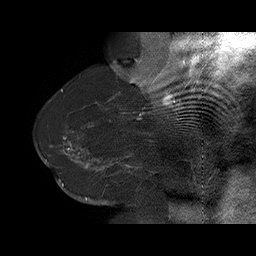
Breast MRI (dynamic contrast-enhanced), one sagittal slice. Slice 48 of 75 in the series (ordered by position). Dynamic contrast-enhanced series, time point 2 of 6 at this slice position (early post-contrast). 1.5 T. TE 4.5 ms, TR 32.4 ms. 3 mm slice thickness. 256 × 256 image matrix, field of view 180 × 180 mm. Female patient. From the clinical record (not read from this slice): setting: breast cancer imaged before/during neoadjuvant chemotherapy; receptor status: HR-positive, HER2-negative.
Annotated regions visible in this slice (semi-automatic segmentation, software-assisted and operator-edited):
- analysis volume of interest (the breast-tissue region the enhancement analysis was run in; not a lesion): bounding box <58,134,166,191> (left, top, right, bottom; pixels)
- tumour enhancement mask (voxels above the 100 % enhancement threshold inside the analysis volume of interest): <64,137,140,170>